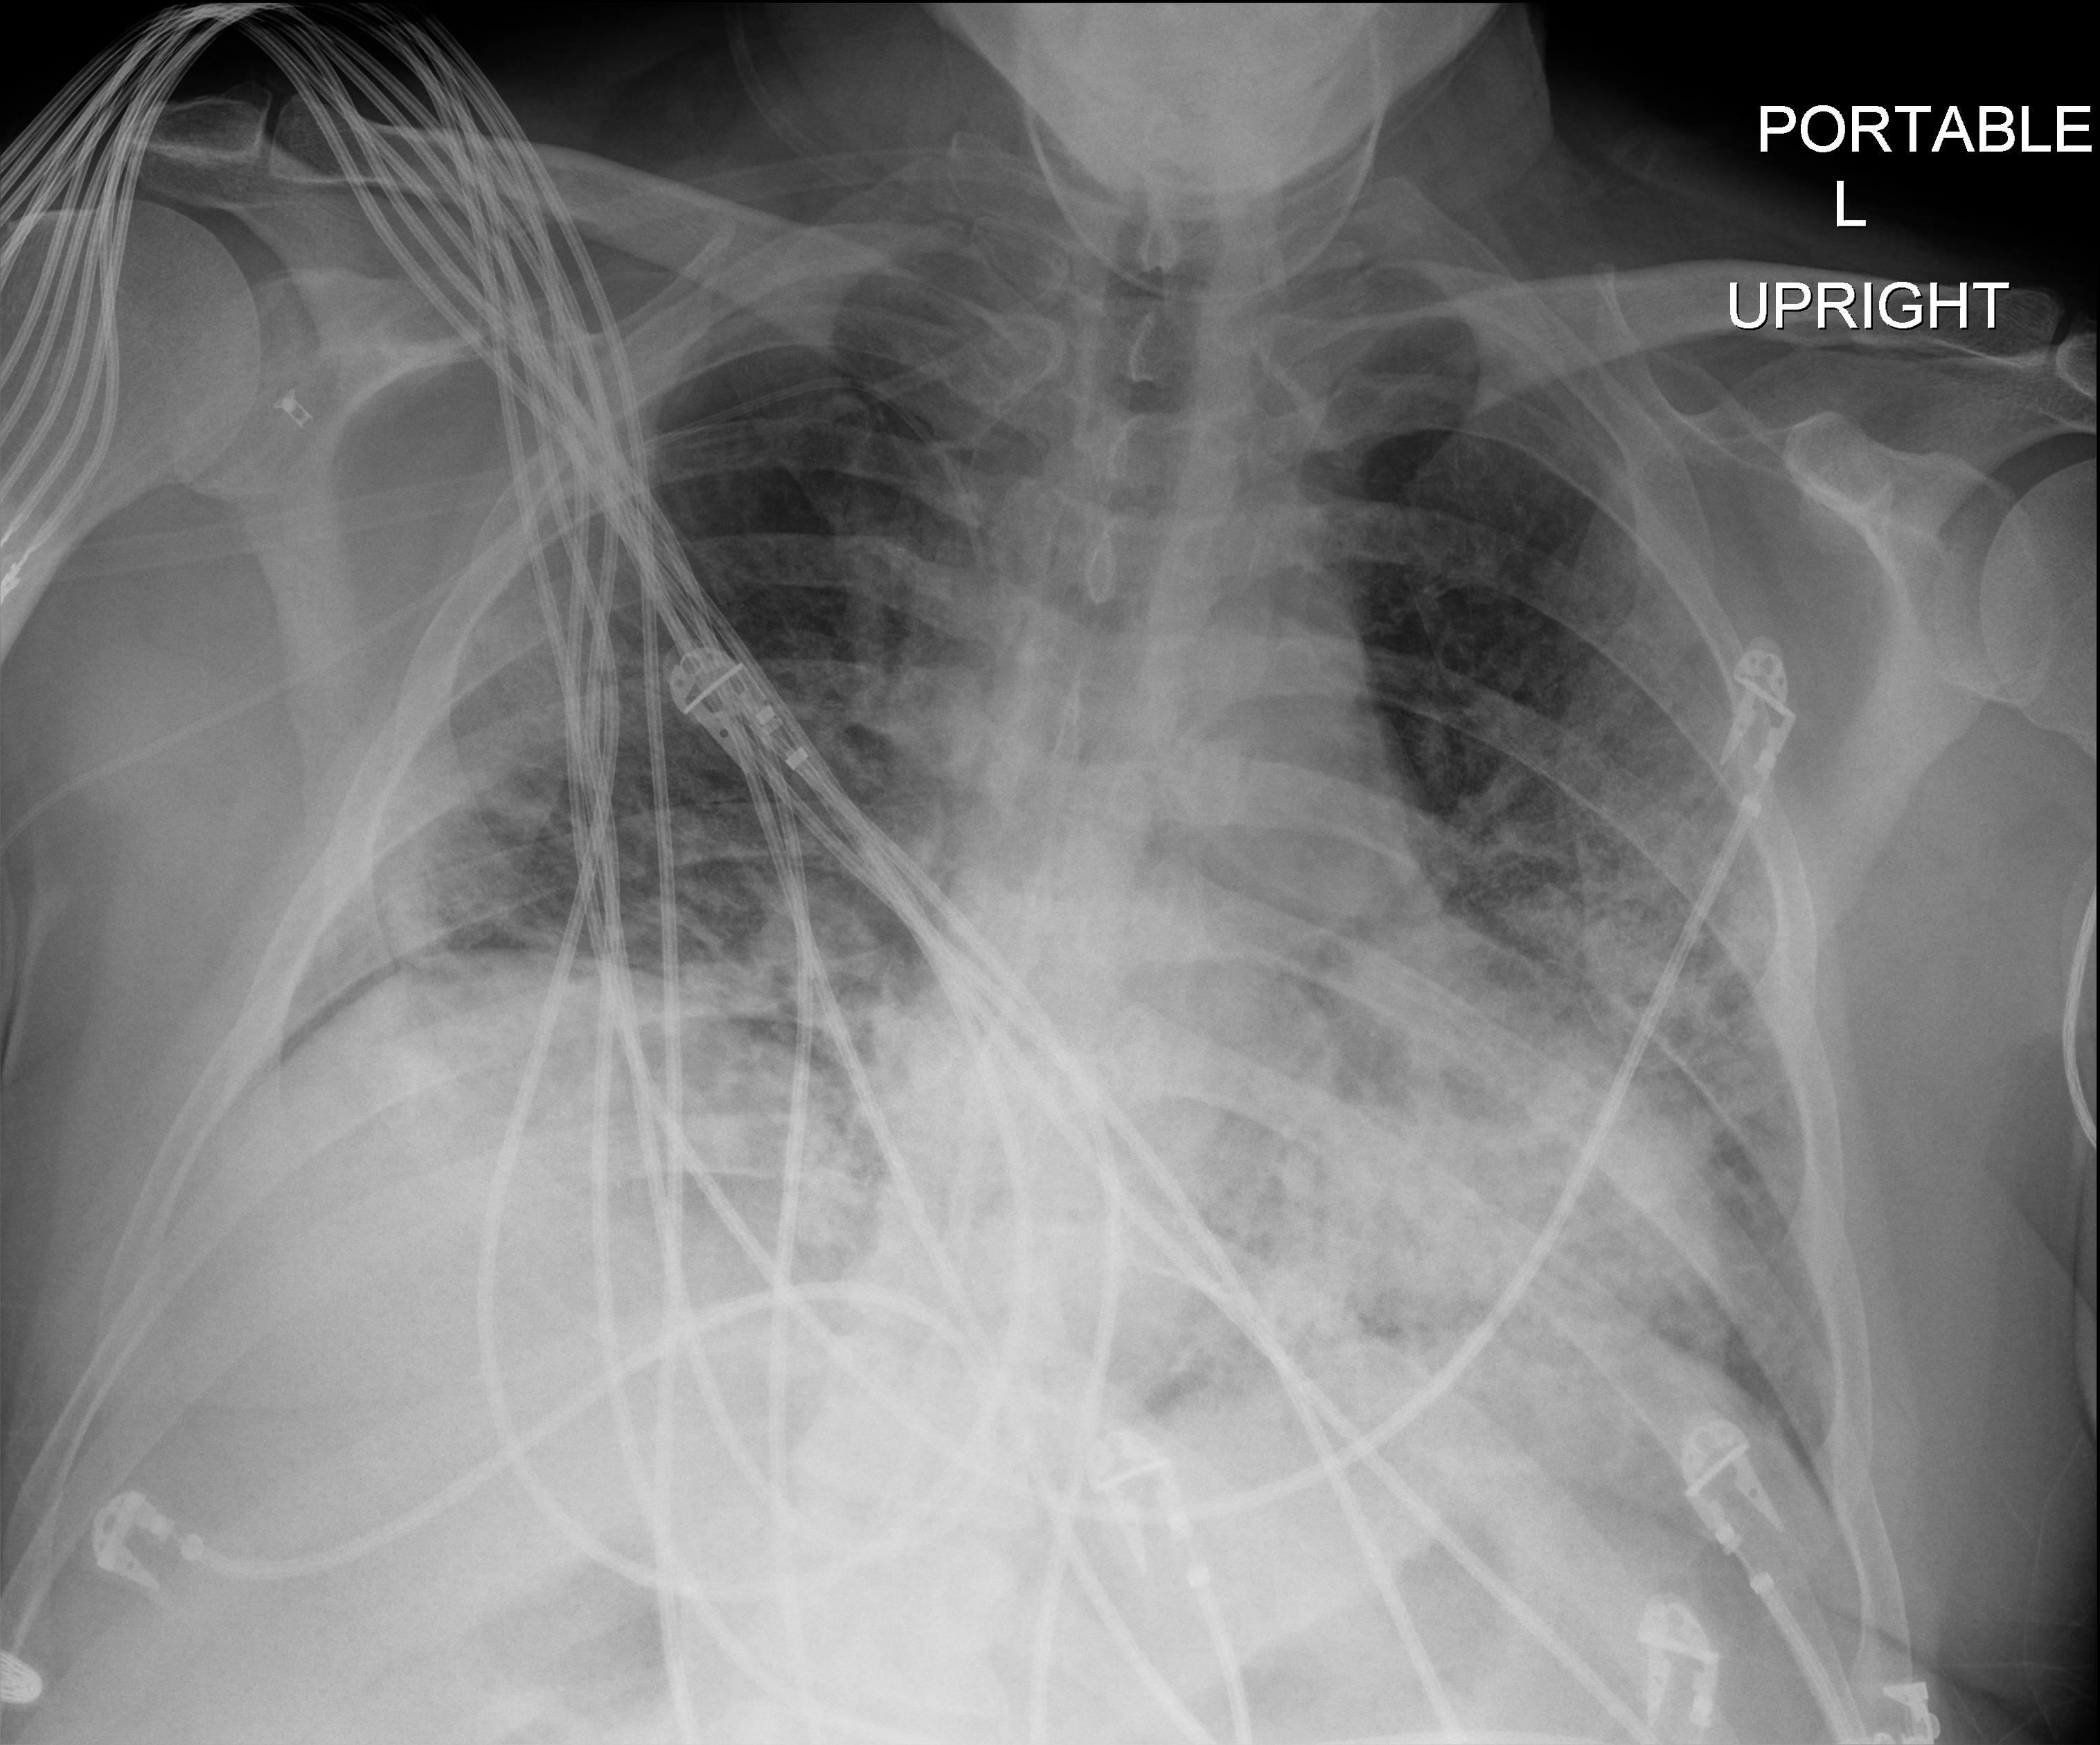
Chest X-ray (portable); anteroposterior (AP) projection. Male patient hospitalised with COVID-19, age 18–59 years.
Hospital-stay facts (about this admission, not read from this image; timing relative to this image not recorded): admitted to intensive care during this hospital stay: yes.